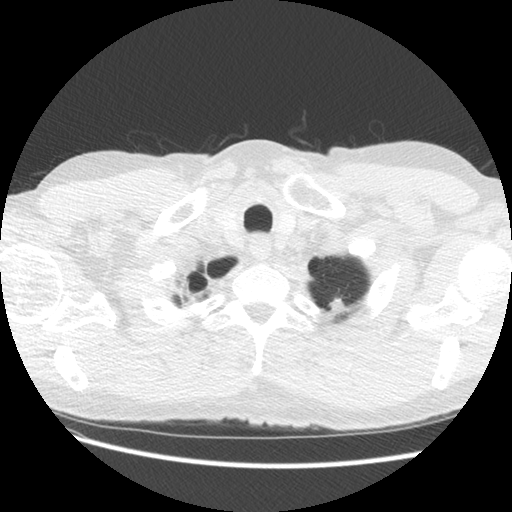
Low-dose screening chest CT, one axial slice; position 120 of 131 along the scan axis; reconstruction kernel STANDARD; 140 kVp; lung window (W 1500 / L -600 HU); 2.5 mm slice thickness; 512 × 512 image matrix.
Structures marked on this image (outlined manually by an expert reader):
- lesion 1 (tumor, upper lobe of left lung): bounding box (x1, y1, x2, y2) in pixels: (328, 298, 345, 314)